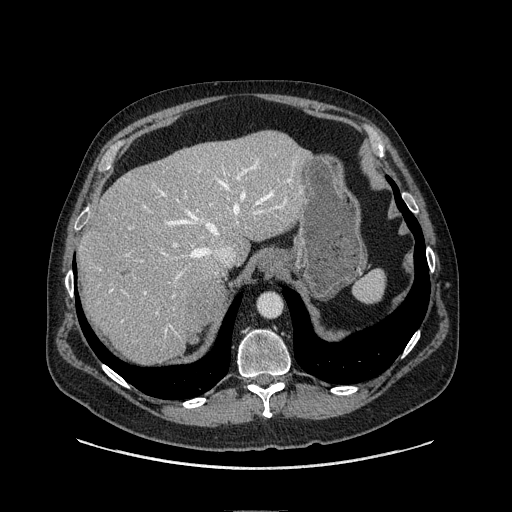
Contrast-enhanced abdominal CT, one axial slice; soft-tissue window (W 400 / L 40 HU); 512 × 512 image matrix, field of view 440 × 440 mm. Male patient. From the clinical record (not read from this slice): diagnosis: adrenocortical carcinoma; tumour side: right adrenal.
Outlined on this slice (semi-automatic segmentation, software-assisted and operator-edited):
- mass: box from (x=187, y=277) to (x=222, y=338) px